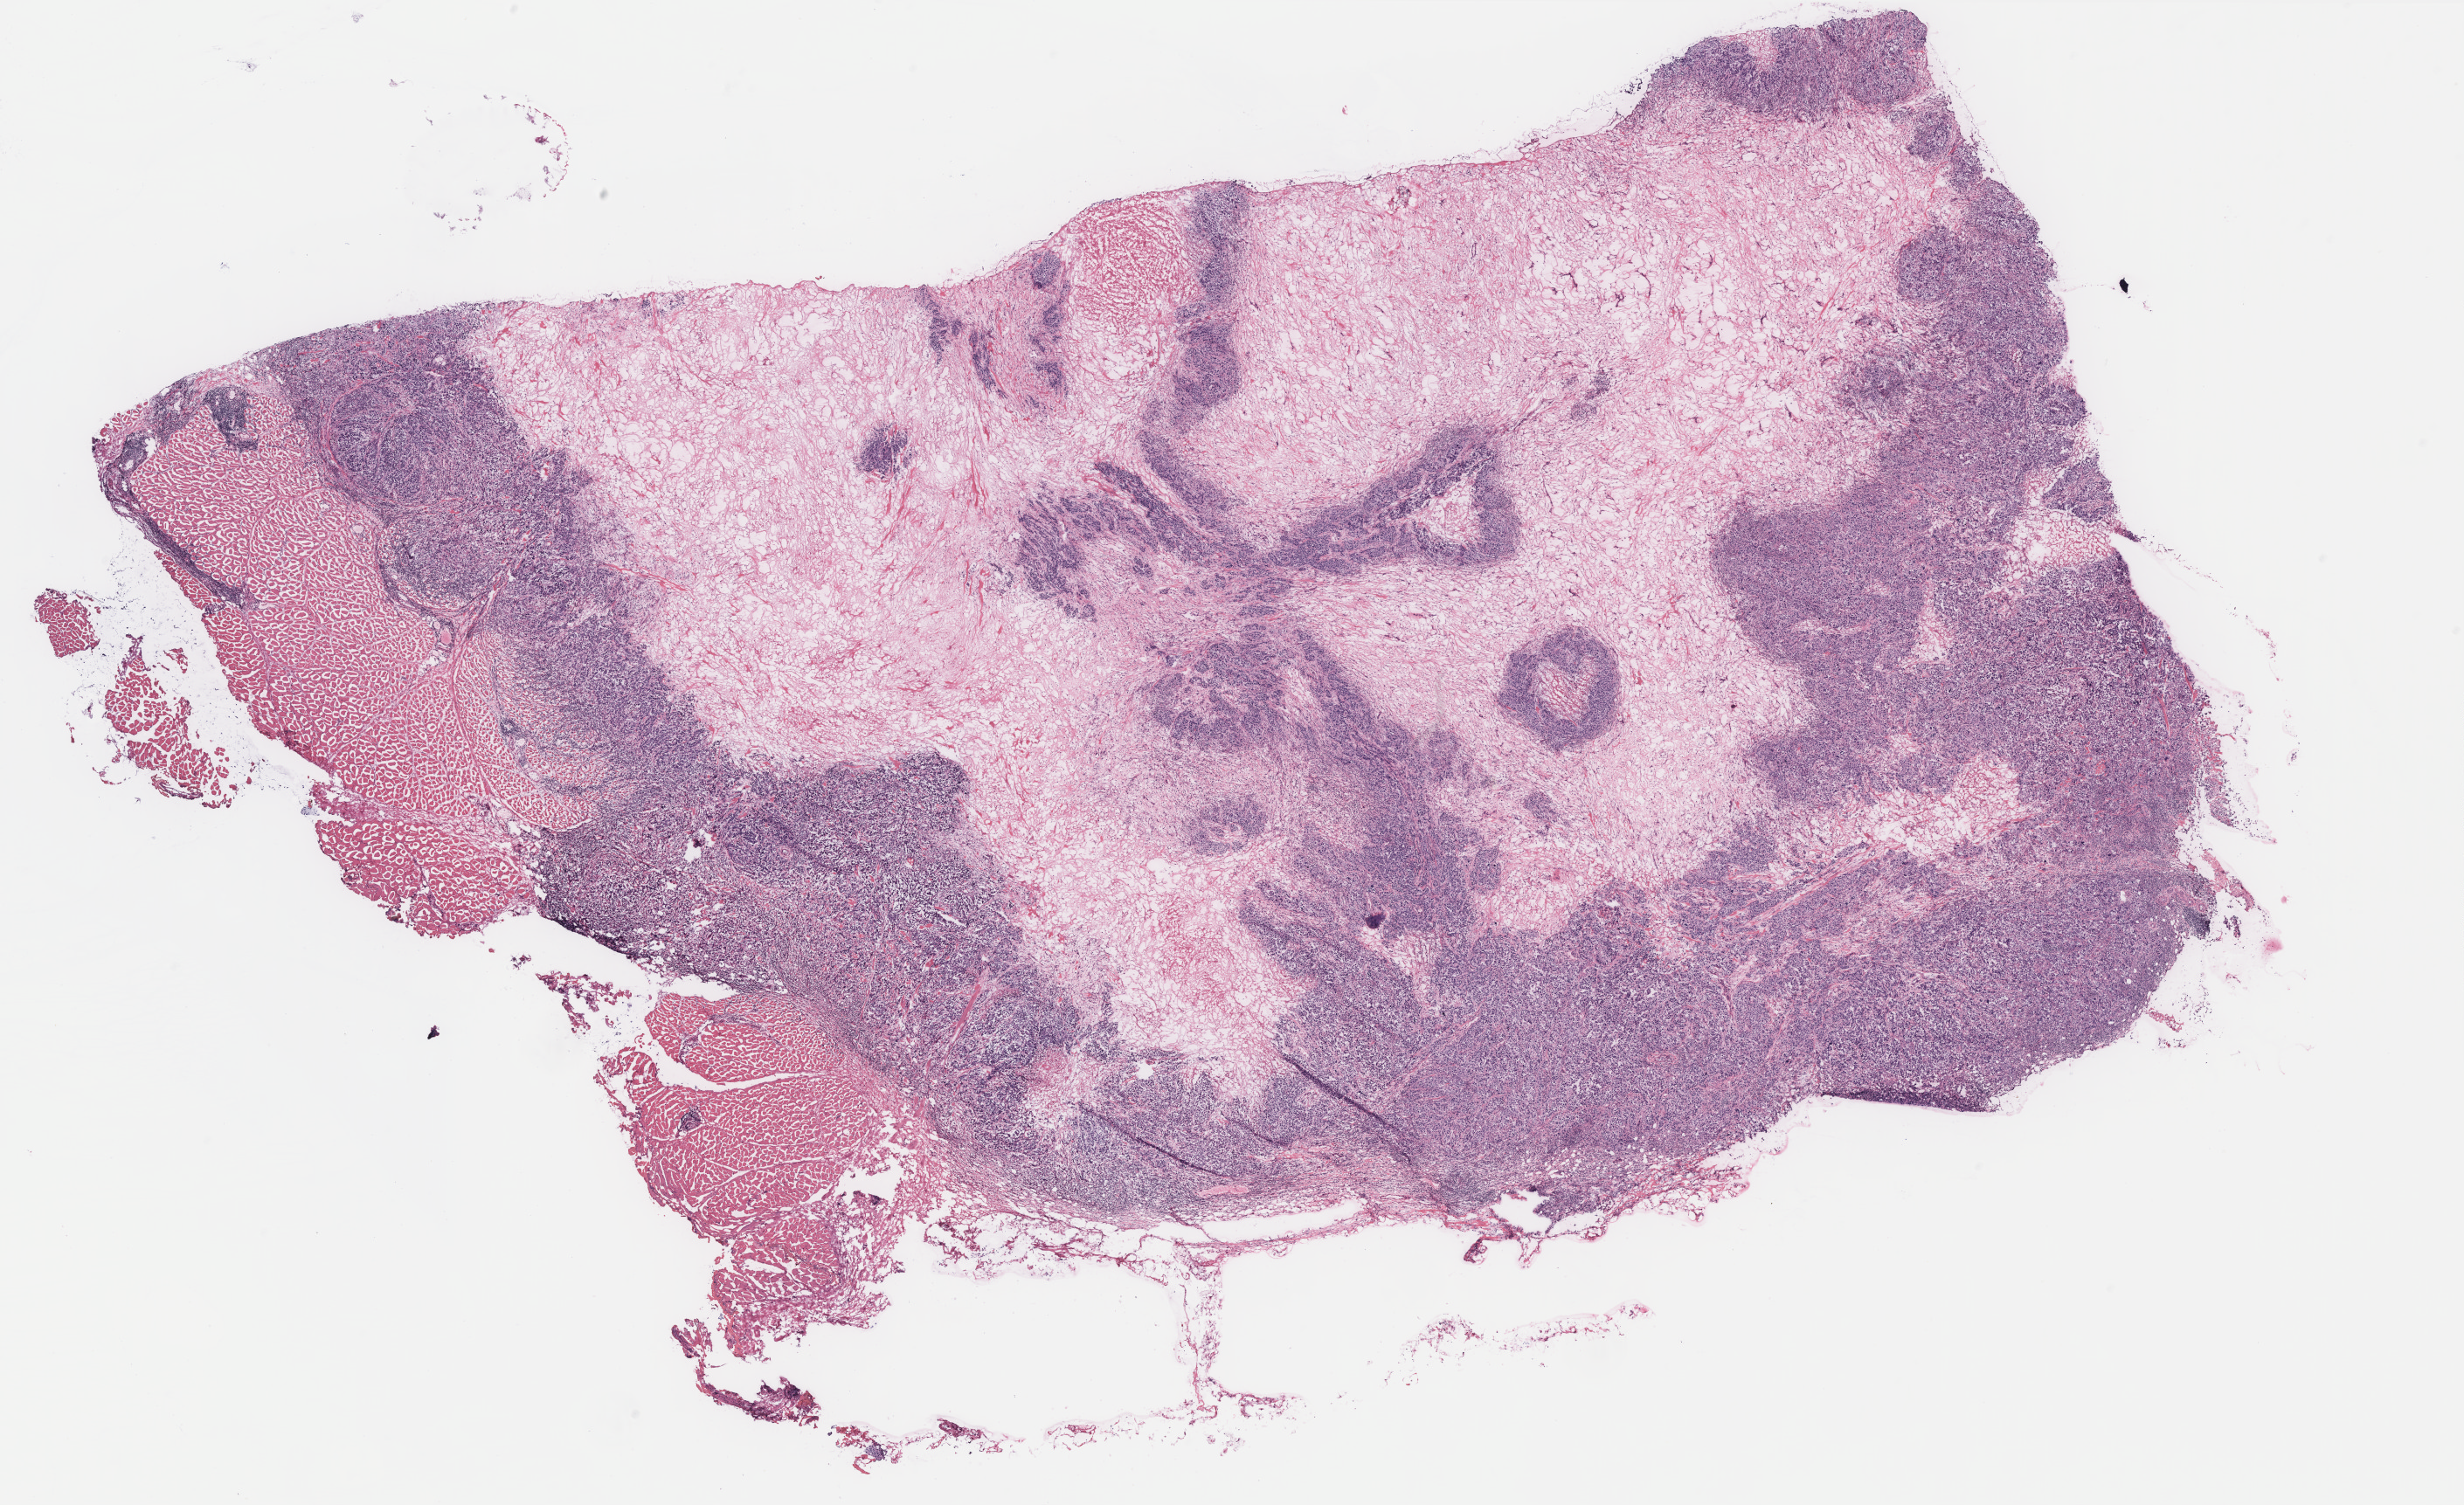
H&E whole-slide image — whole scanned area (about 22.6 x 13.8 mm, from a 40x scan) shown as a low-resolution overview, breast, tumour tissue. Patient: female, age 68 years.
AJCC pathologic stage: IIB. Diagnosis: Infiltrating duct carcinoma, NOS.